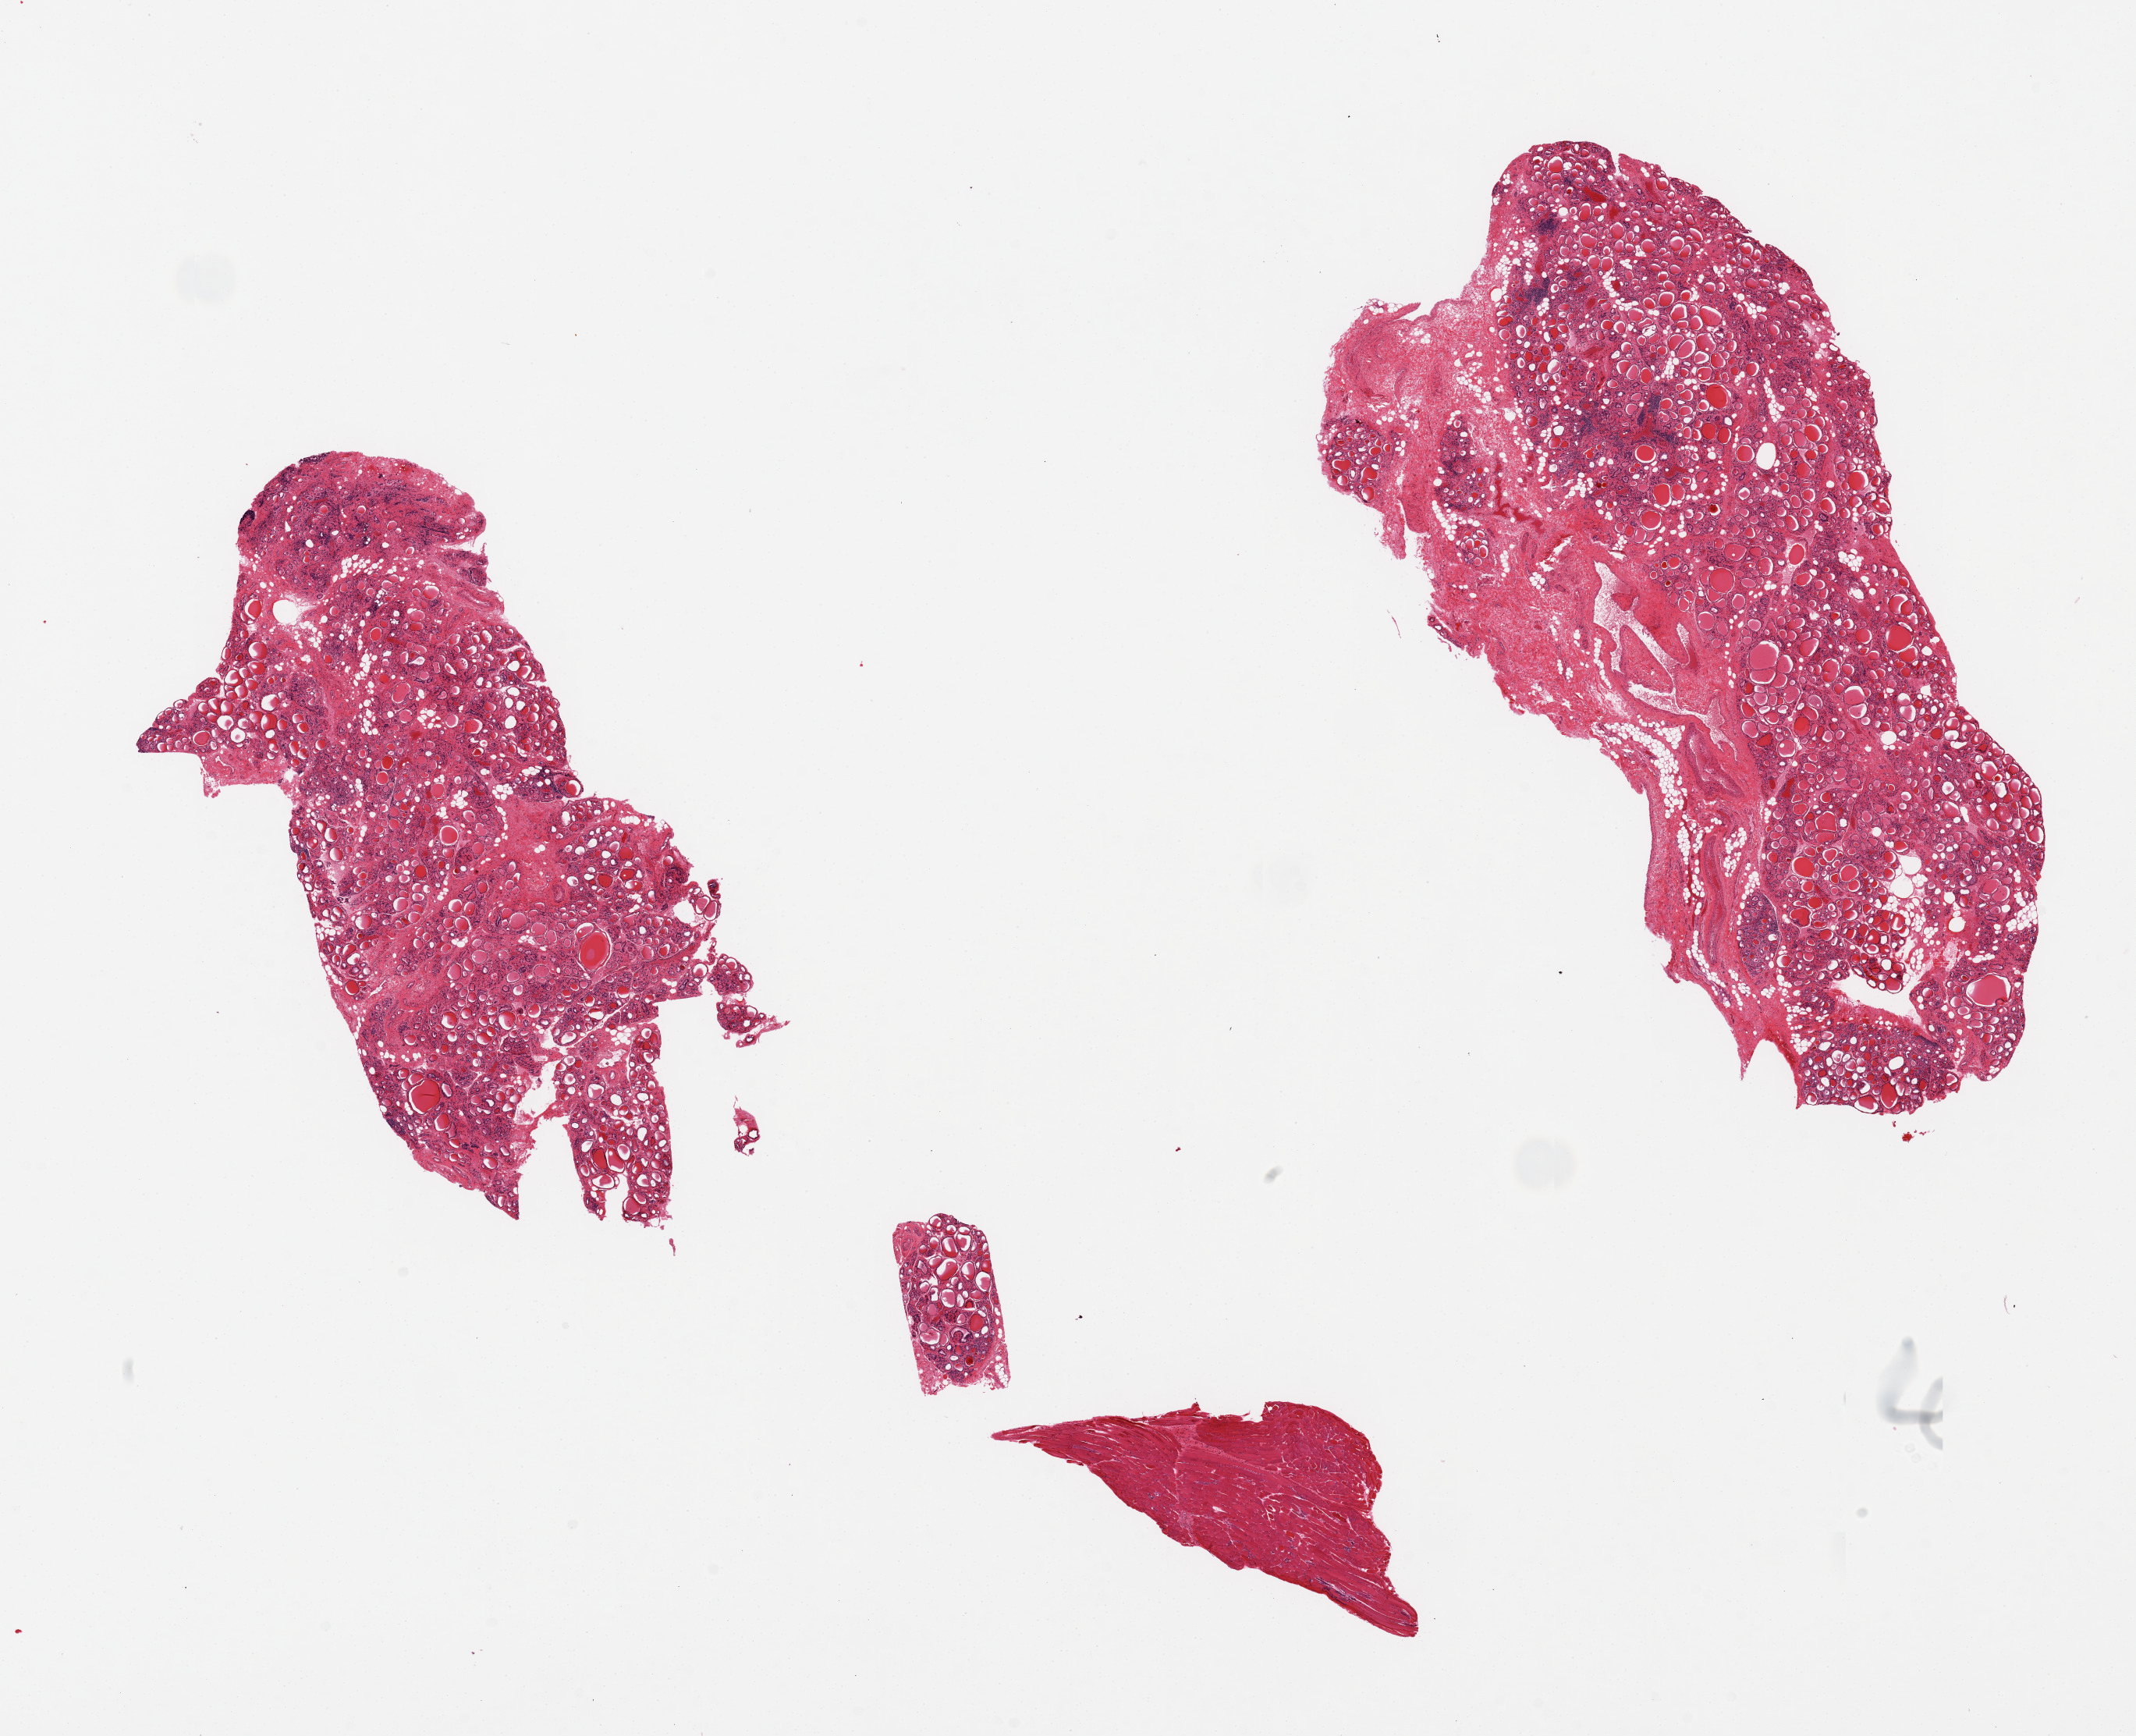
Digitized hematoxylin and eosin (H&E)-stained section, shown as a low-resolution overview of the whole scanned area (about 21.7 x 17.6 mm); PAXgene-fixed, paraffin-embedded tissue; section of thyroid (target tissue); tissue donor sample. Female donor.
Reviewer comment on this tissue sample: 4 pieces, one is skeletal muscle, one is 30% vessels/fibrofatty tissue, patchy chronic inflammation and fibrosis.